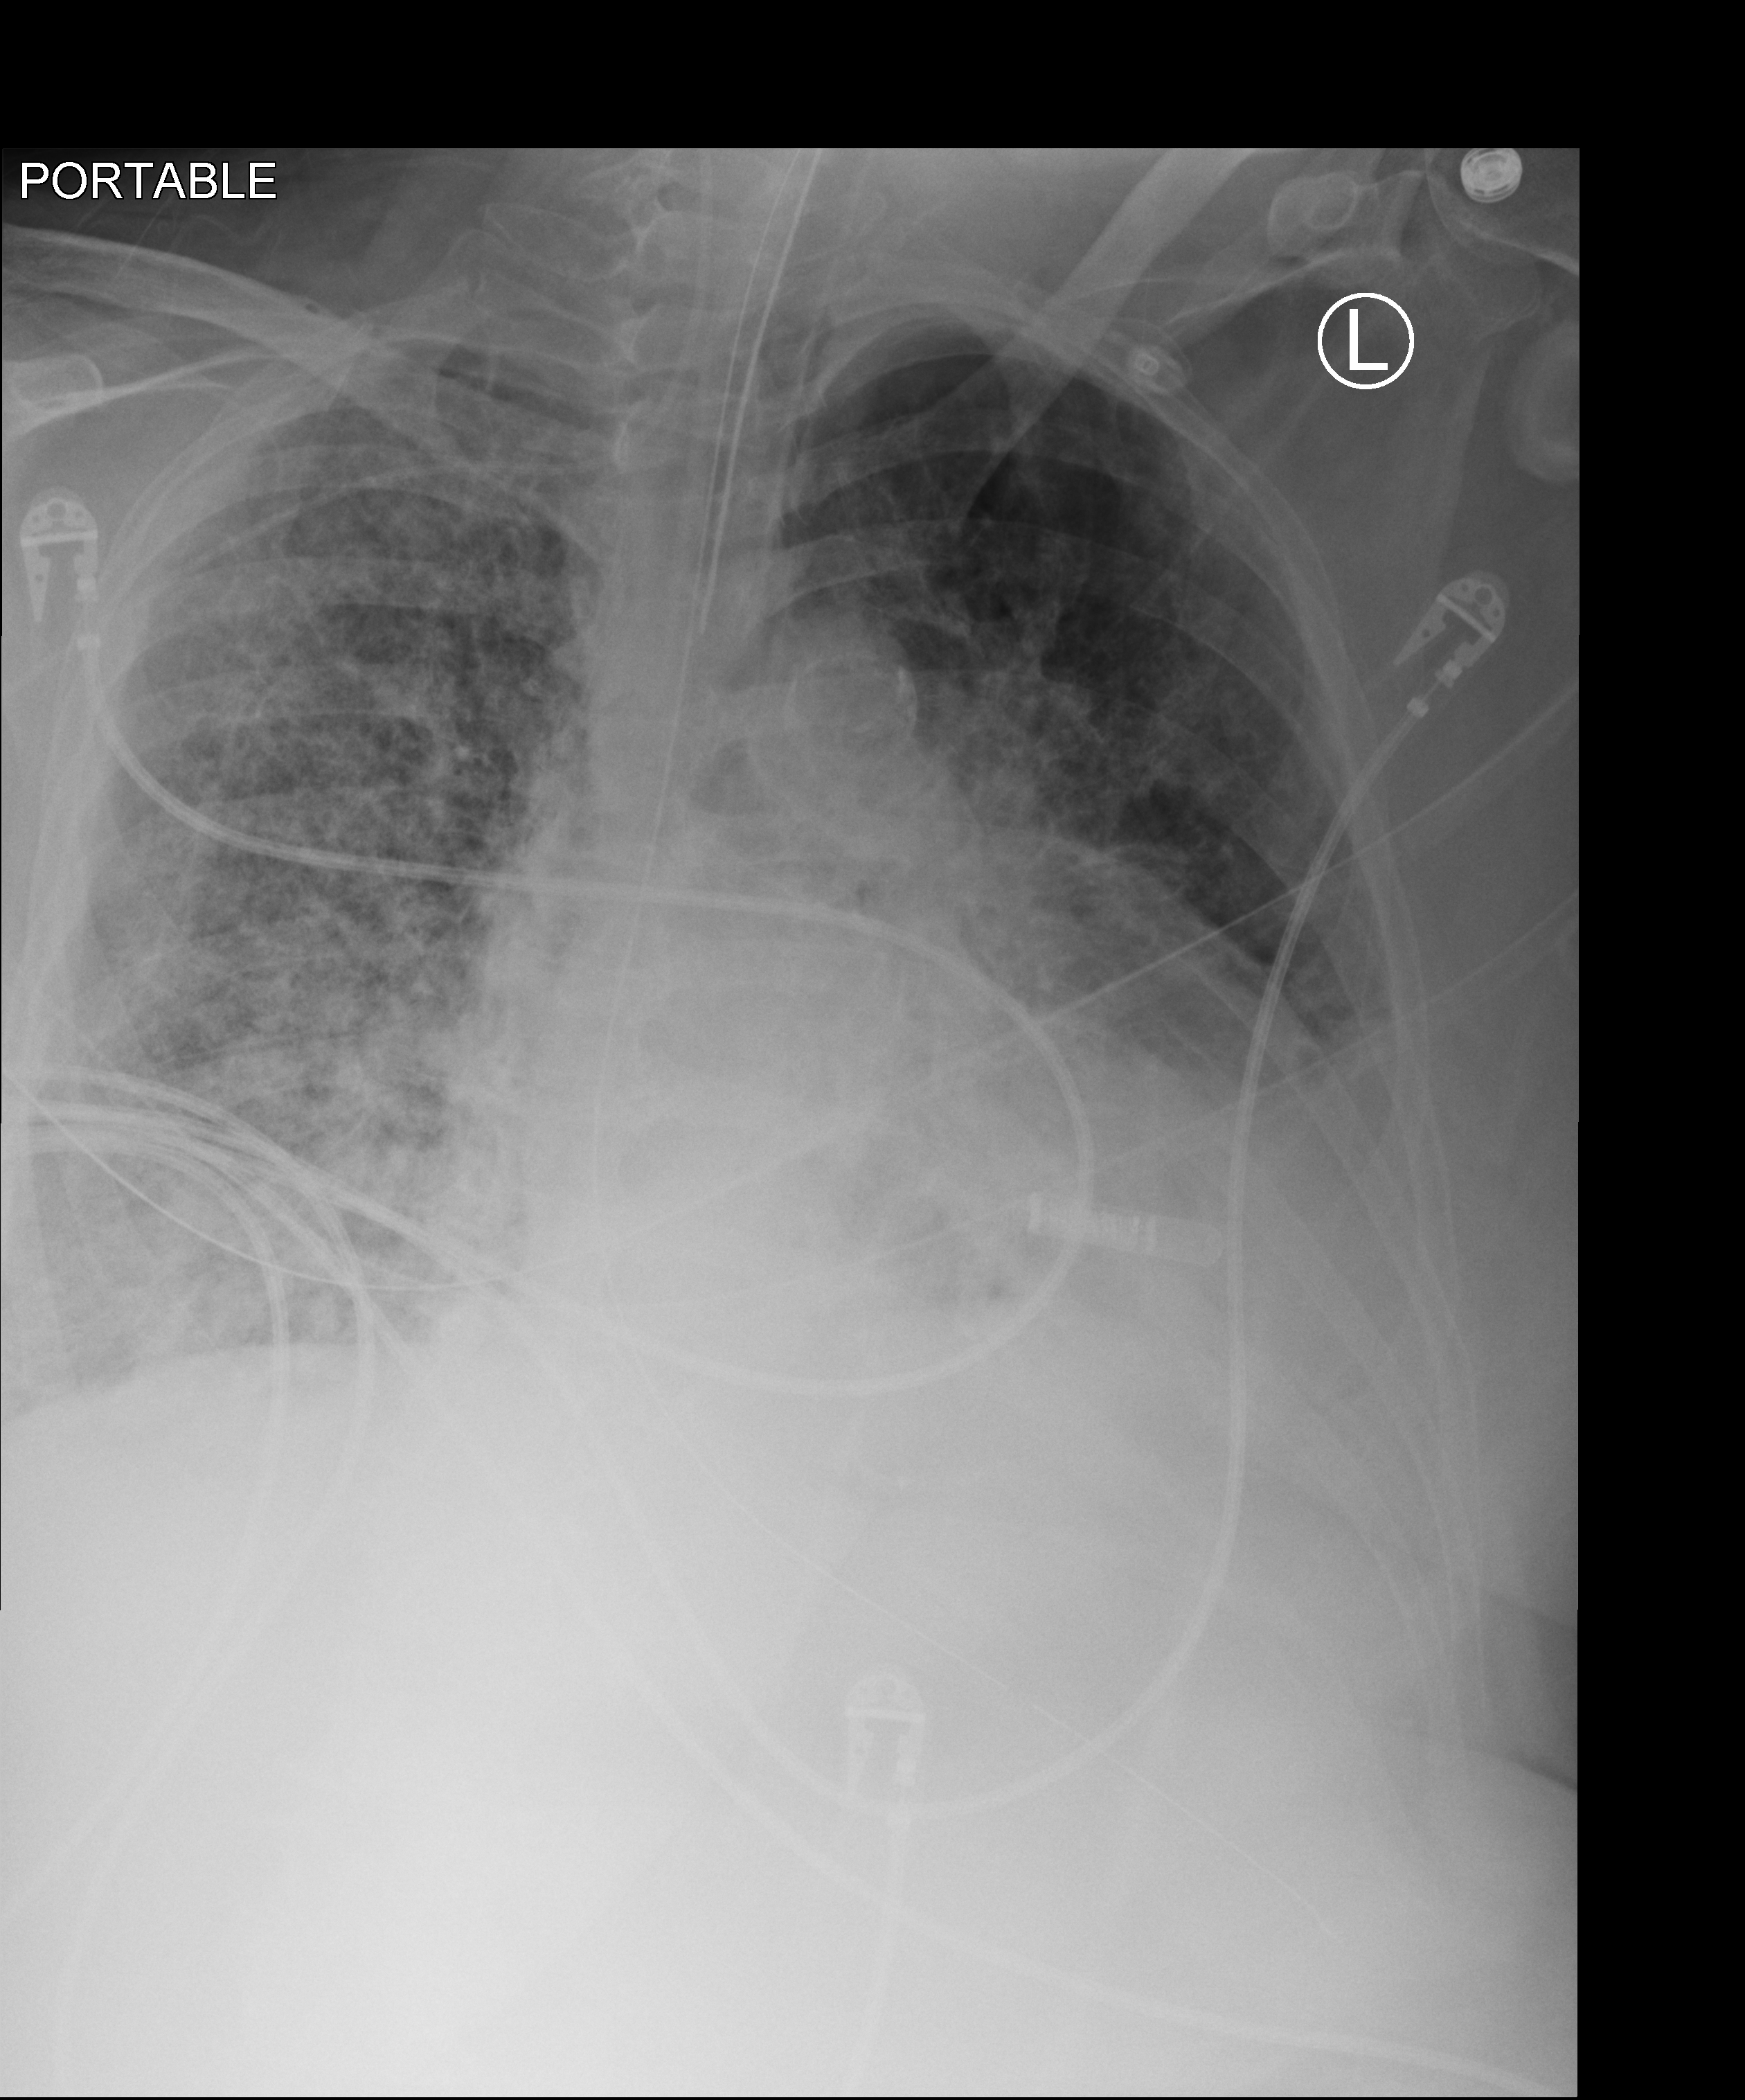
Chest X-ray (portable); anteroposterior (AP) projection. Female patient hospitalised with COVID-19, age 60–74 years.
Admission-level facts for this patient (not findings on this image; timing relative to this image not recorded): hypertension (admission record): yes; length of hospital stay: 28 days; admitted to intensive care during this hospital stay: yes.